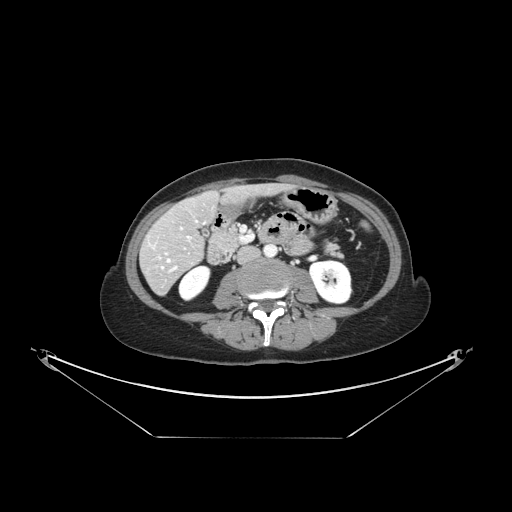
Contrast-enhanced abdominal CT, one axial slice. Position 48 of 148 along the scan axis. 120 kVp. Intravenous contrast given. Soft-tissue window (W 400 / L 40 HU). 2.5 mm slice thickness. 512 × 512 image matrix. Female patient, age 73 years. Case-level facts recorded for this patient, not image findings: diagnosis: colorectal cancer liver metastases, imaged before liver resection; multiple liver metastases: no; largest metastasis: 1 cm; disease in both lobes: no.
Annotated regions visible in this slice (expert manual segmentation):
- hepatic veins: bounding box <151,221,197,271> (left, top, right, bottom; pixels)
- liver: <143,185,284,294>
- planned liver remnant (the part of the liver to remain after resection): <162,186,283,245>